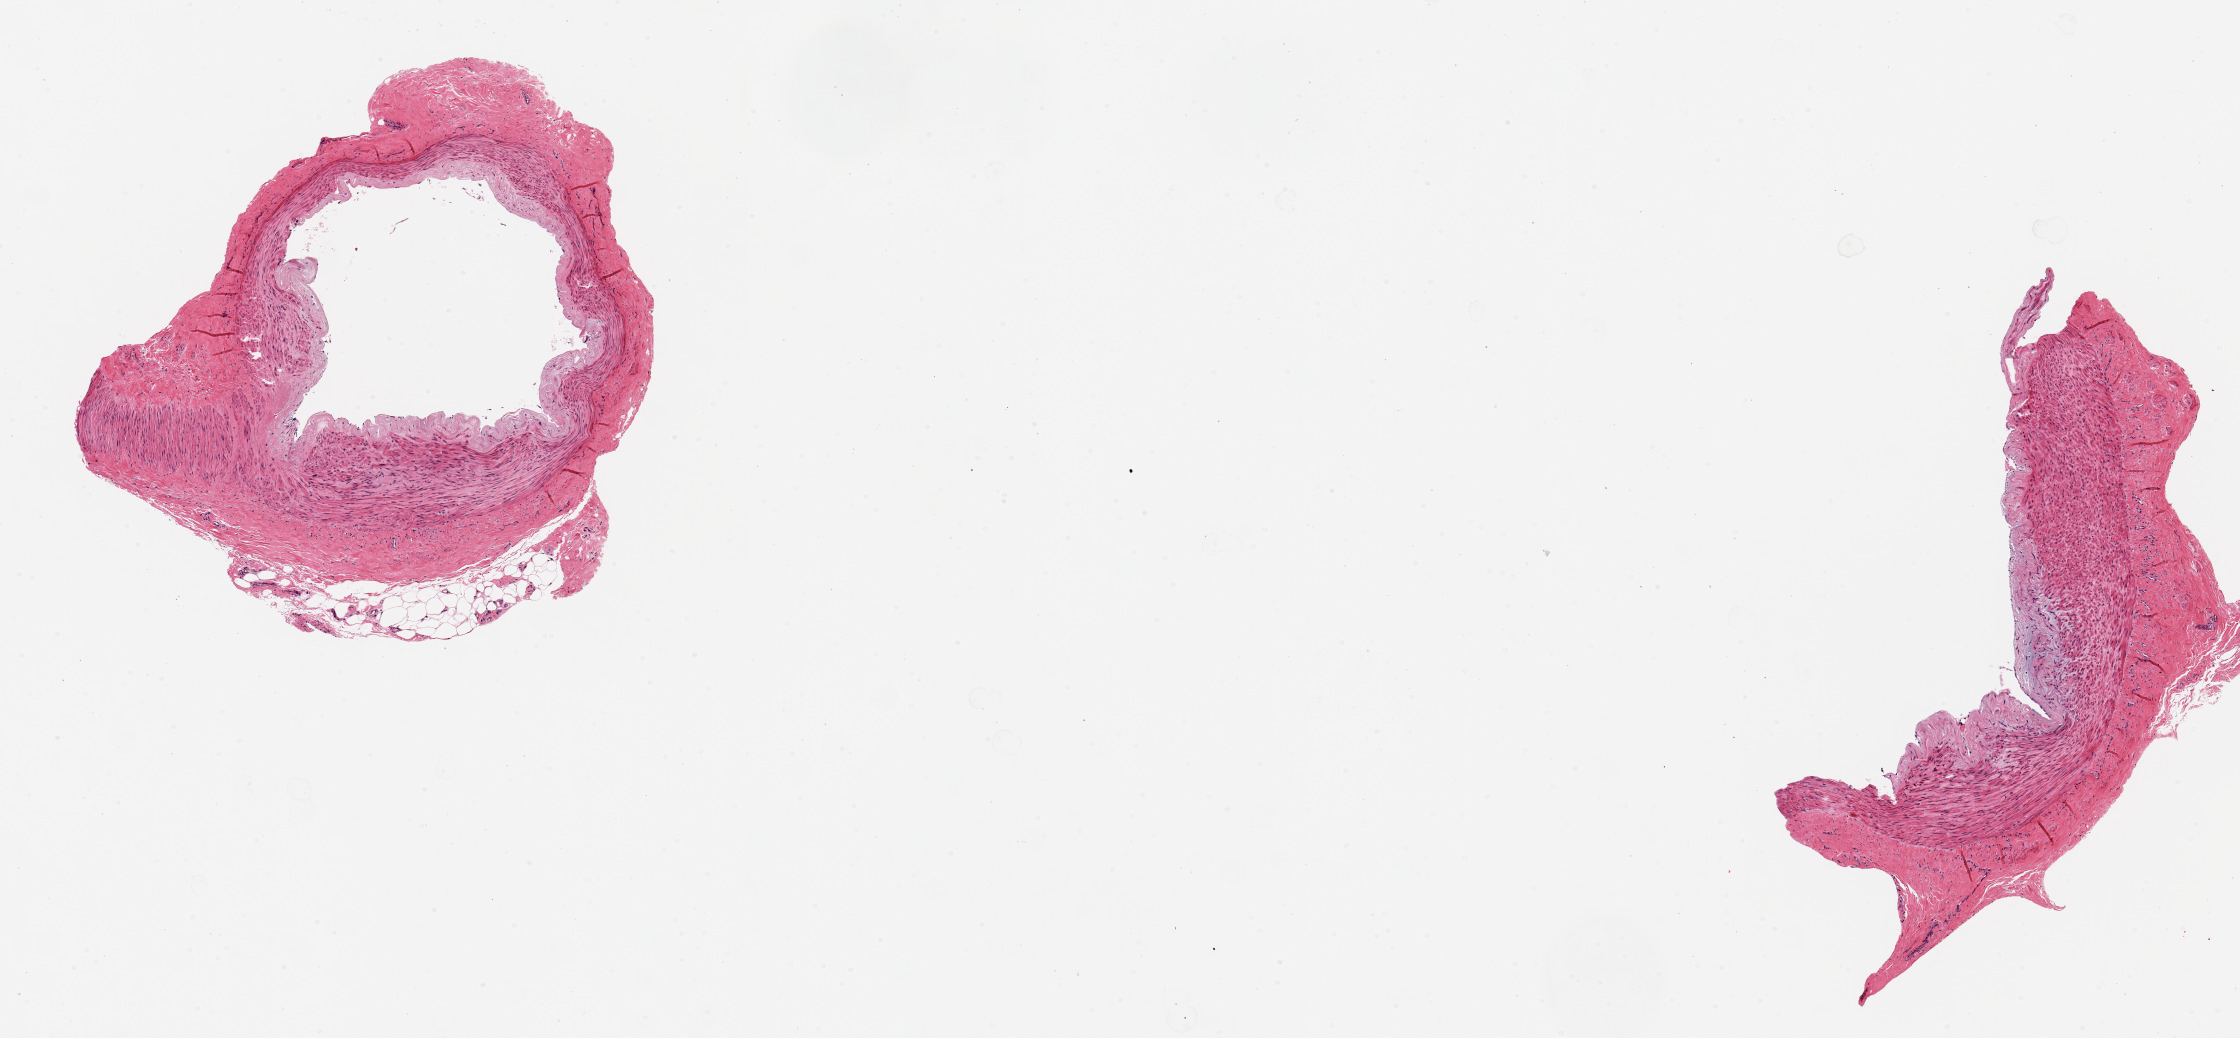
Digitized hematoxylin and eosin (H&E)-stained section, brightfield, whole scanned area (about 8.9 x 4.1 mm, from a 20x scan) shown as a low-resolution overview; PAXgene-fixed, paraffin-embedded tissue; sampled site (target tissue): tibial artery; donor tissue sample. Donor sex: female.
Review note (as recorded): 2 pieces, 2x2 & 2.5x1 mm; <5% adipose.